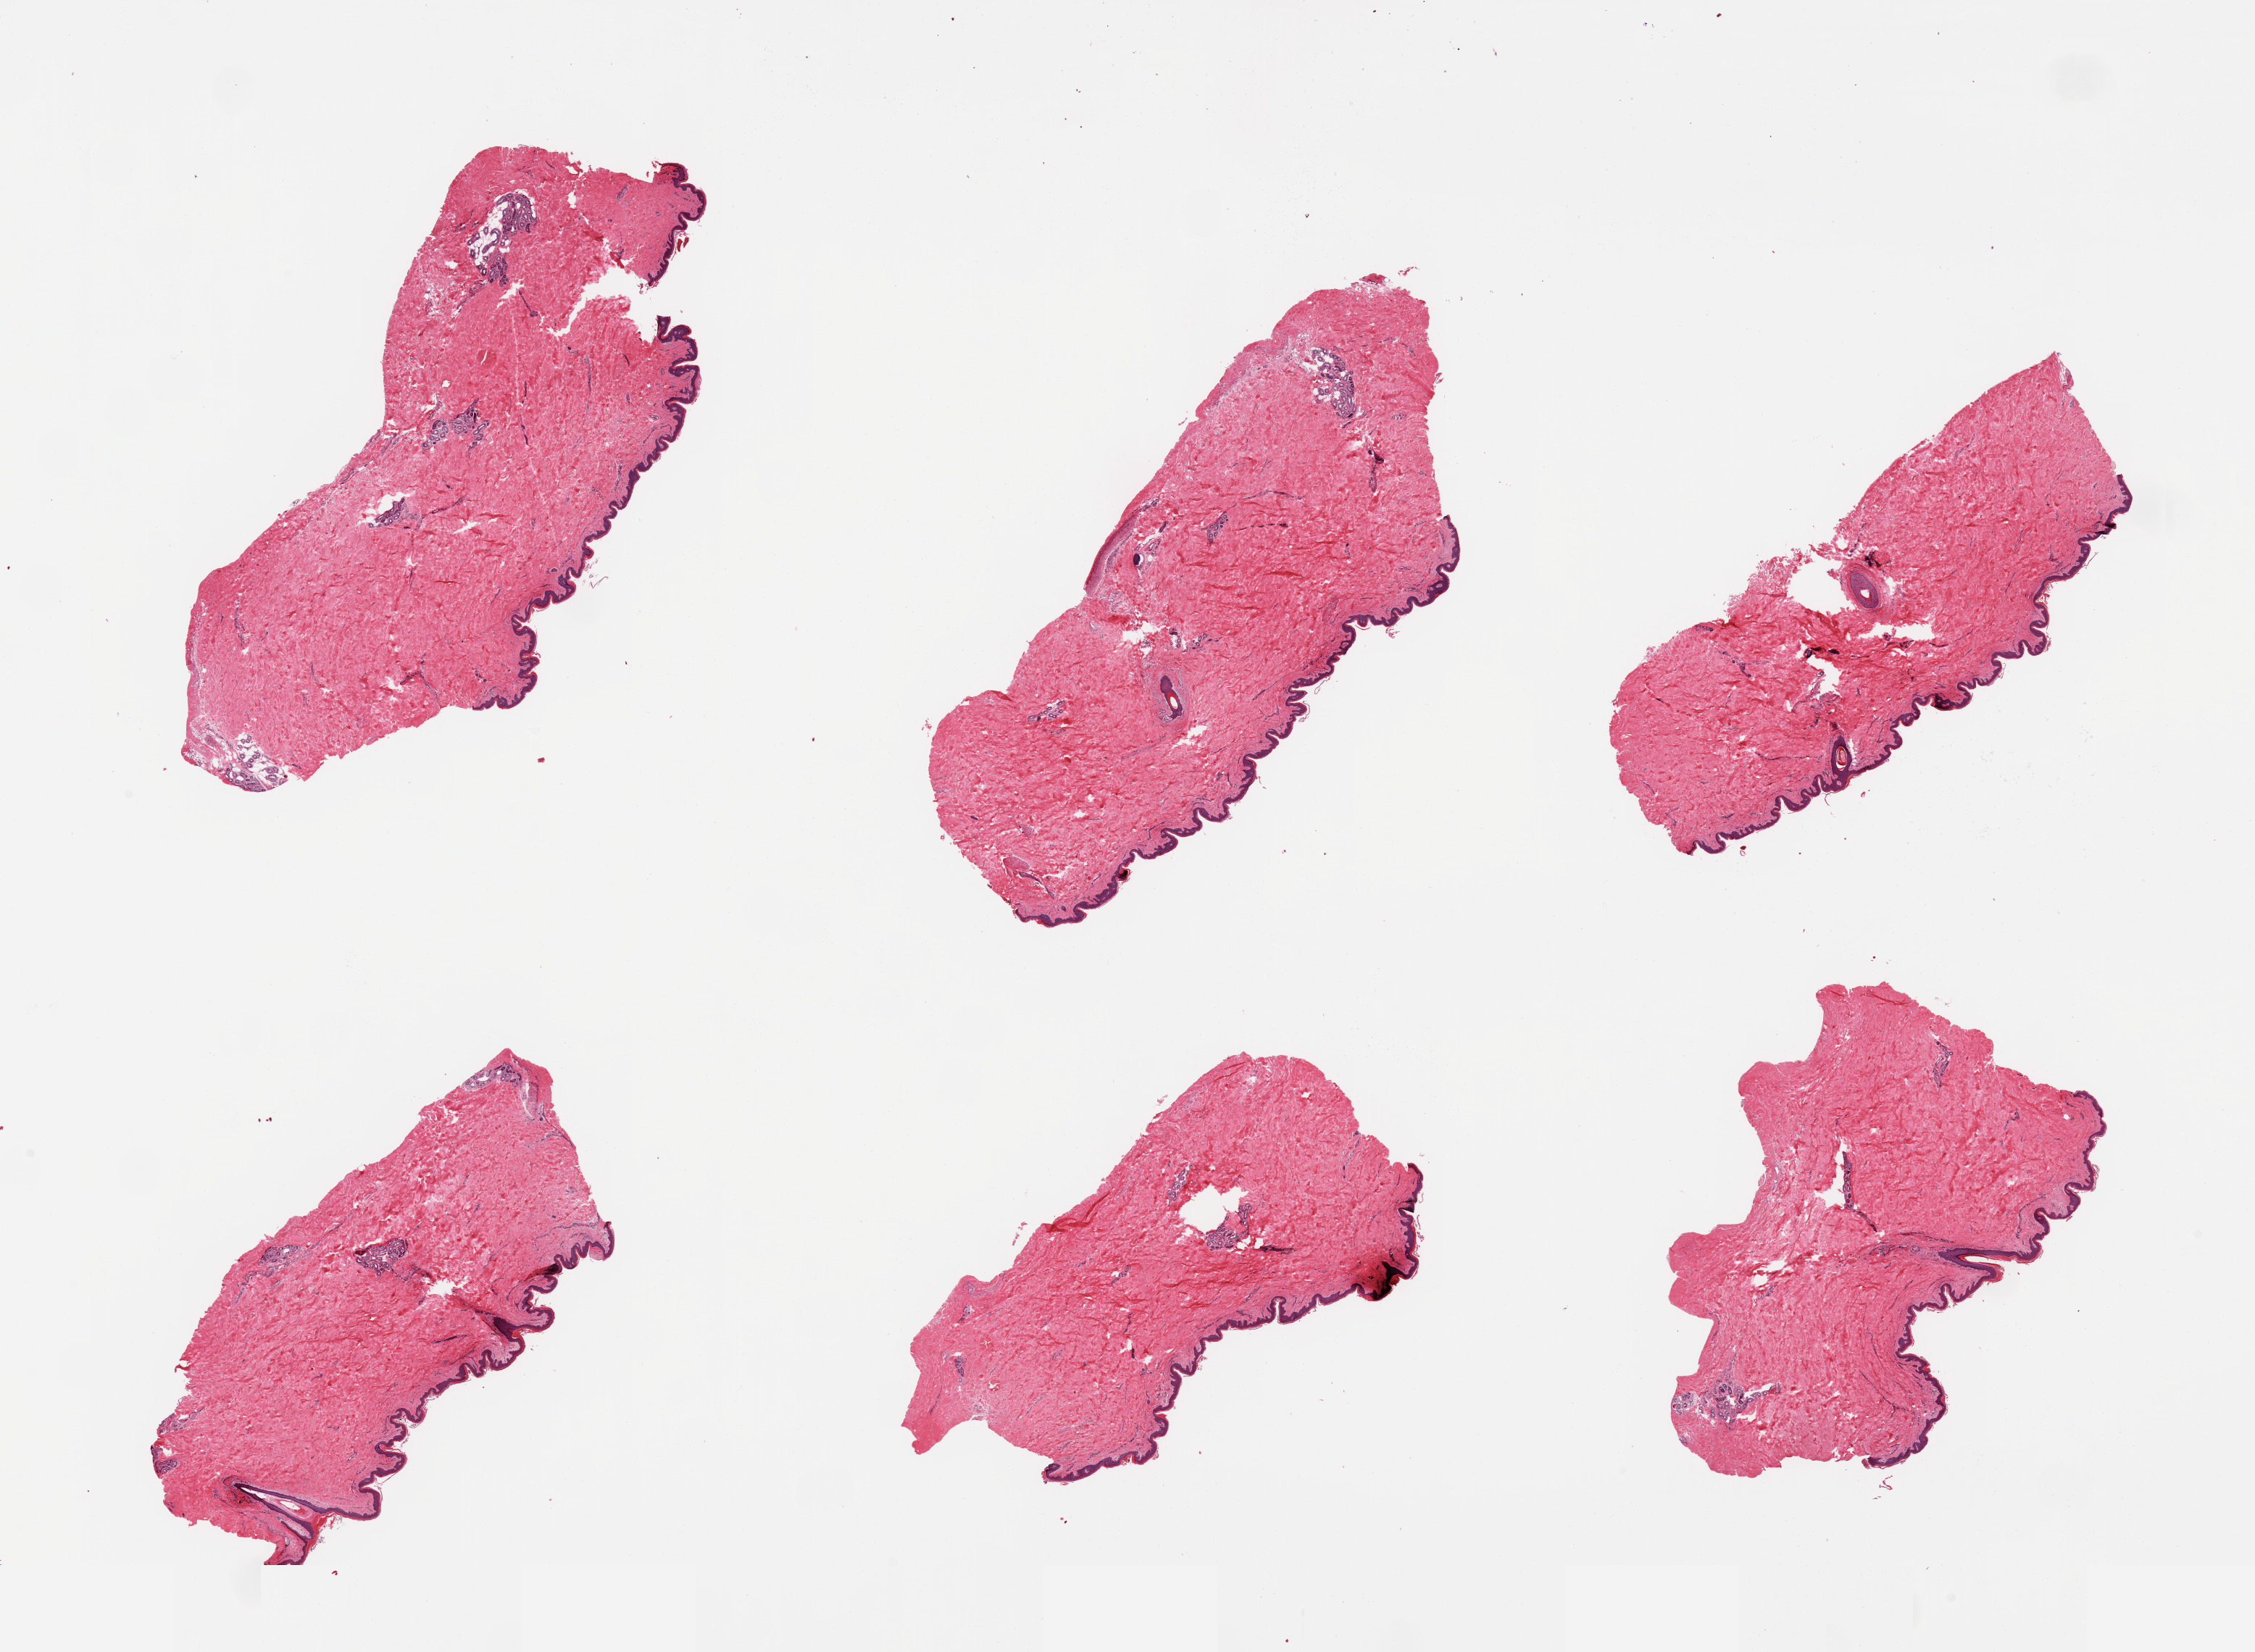
Whole-slide image, hematoxylin and eosin (H&E) stain, brightfield, a low-resolution overview of the entire scanned area, about 24.6 x 18.0 mm, PAXgene-fixed paraffin-embedded (PFPE) section, target tissue: skin of suprapubic region, tissue donor sample.
Review note (as recorded): 6 pieces, minimal dermal fat; squamous epithelium is ~40 microns.